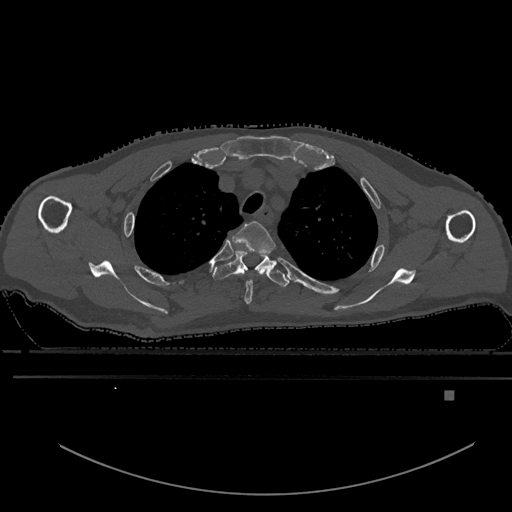
CT including the spine, one axial slice; position 469 of 969 along the scan axis; bone window (W 1800 / L 400 HU); 0.5 mm slice thickness; 512 × 512 image matrix, field of view 456 × 456 mm. Male patient, age 82 years. Case-level facts recorded for this patient, not image findings: primary cancer: prostate; vertebrae with lytic lesions (as recorded): T11, T9, T8, T2.
Structures marked on this image (semi-automatically segmented with operator editing):
- T2 vertebra: bounding box (x1, y1, x2, y2) in pixels: (232, 221, 275, 305)
- T3 vertebra: (212, 251, 289, 287)